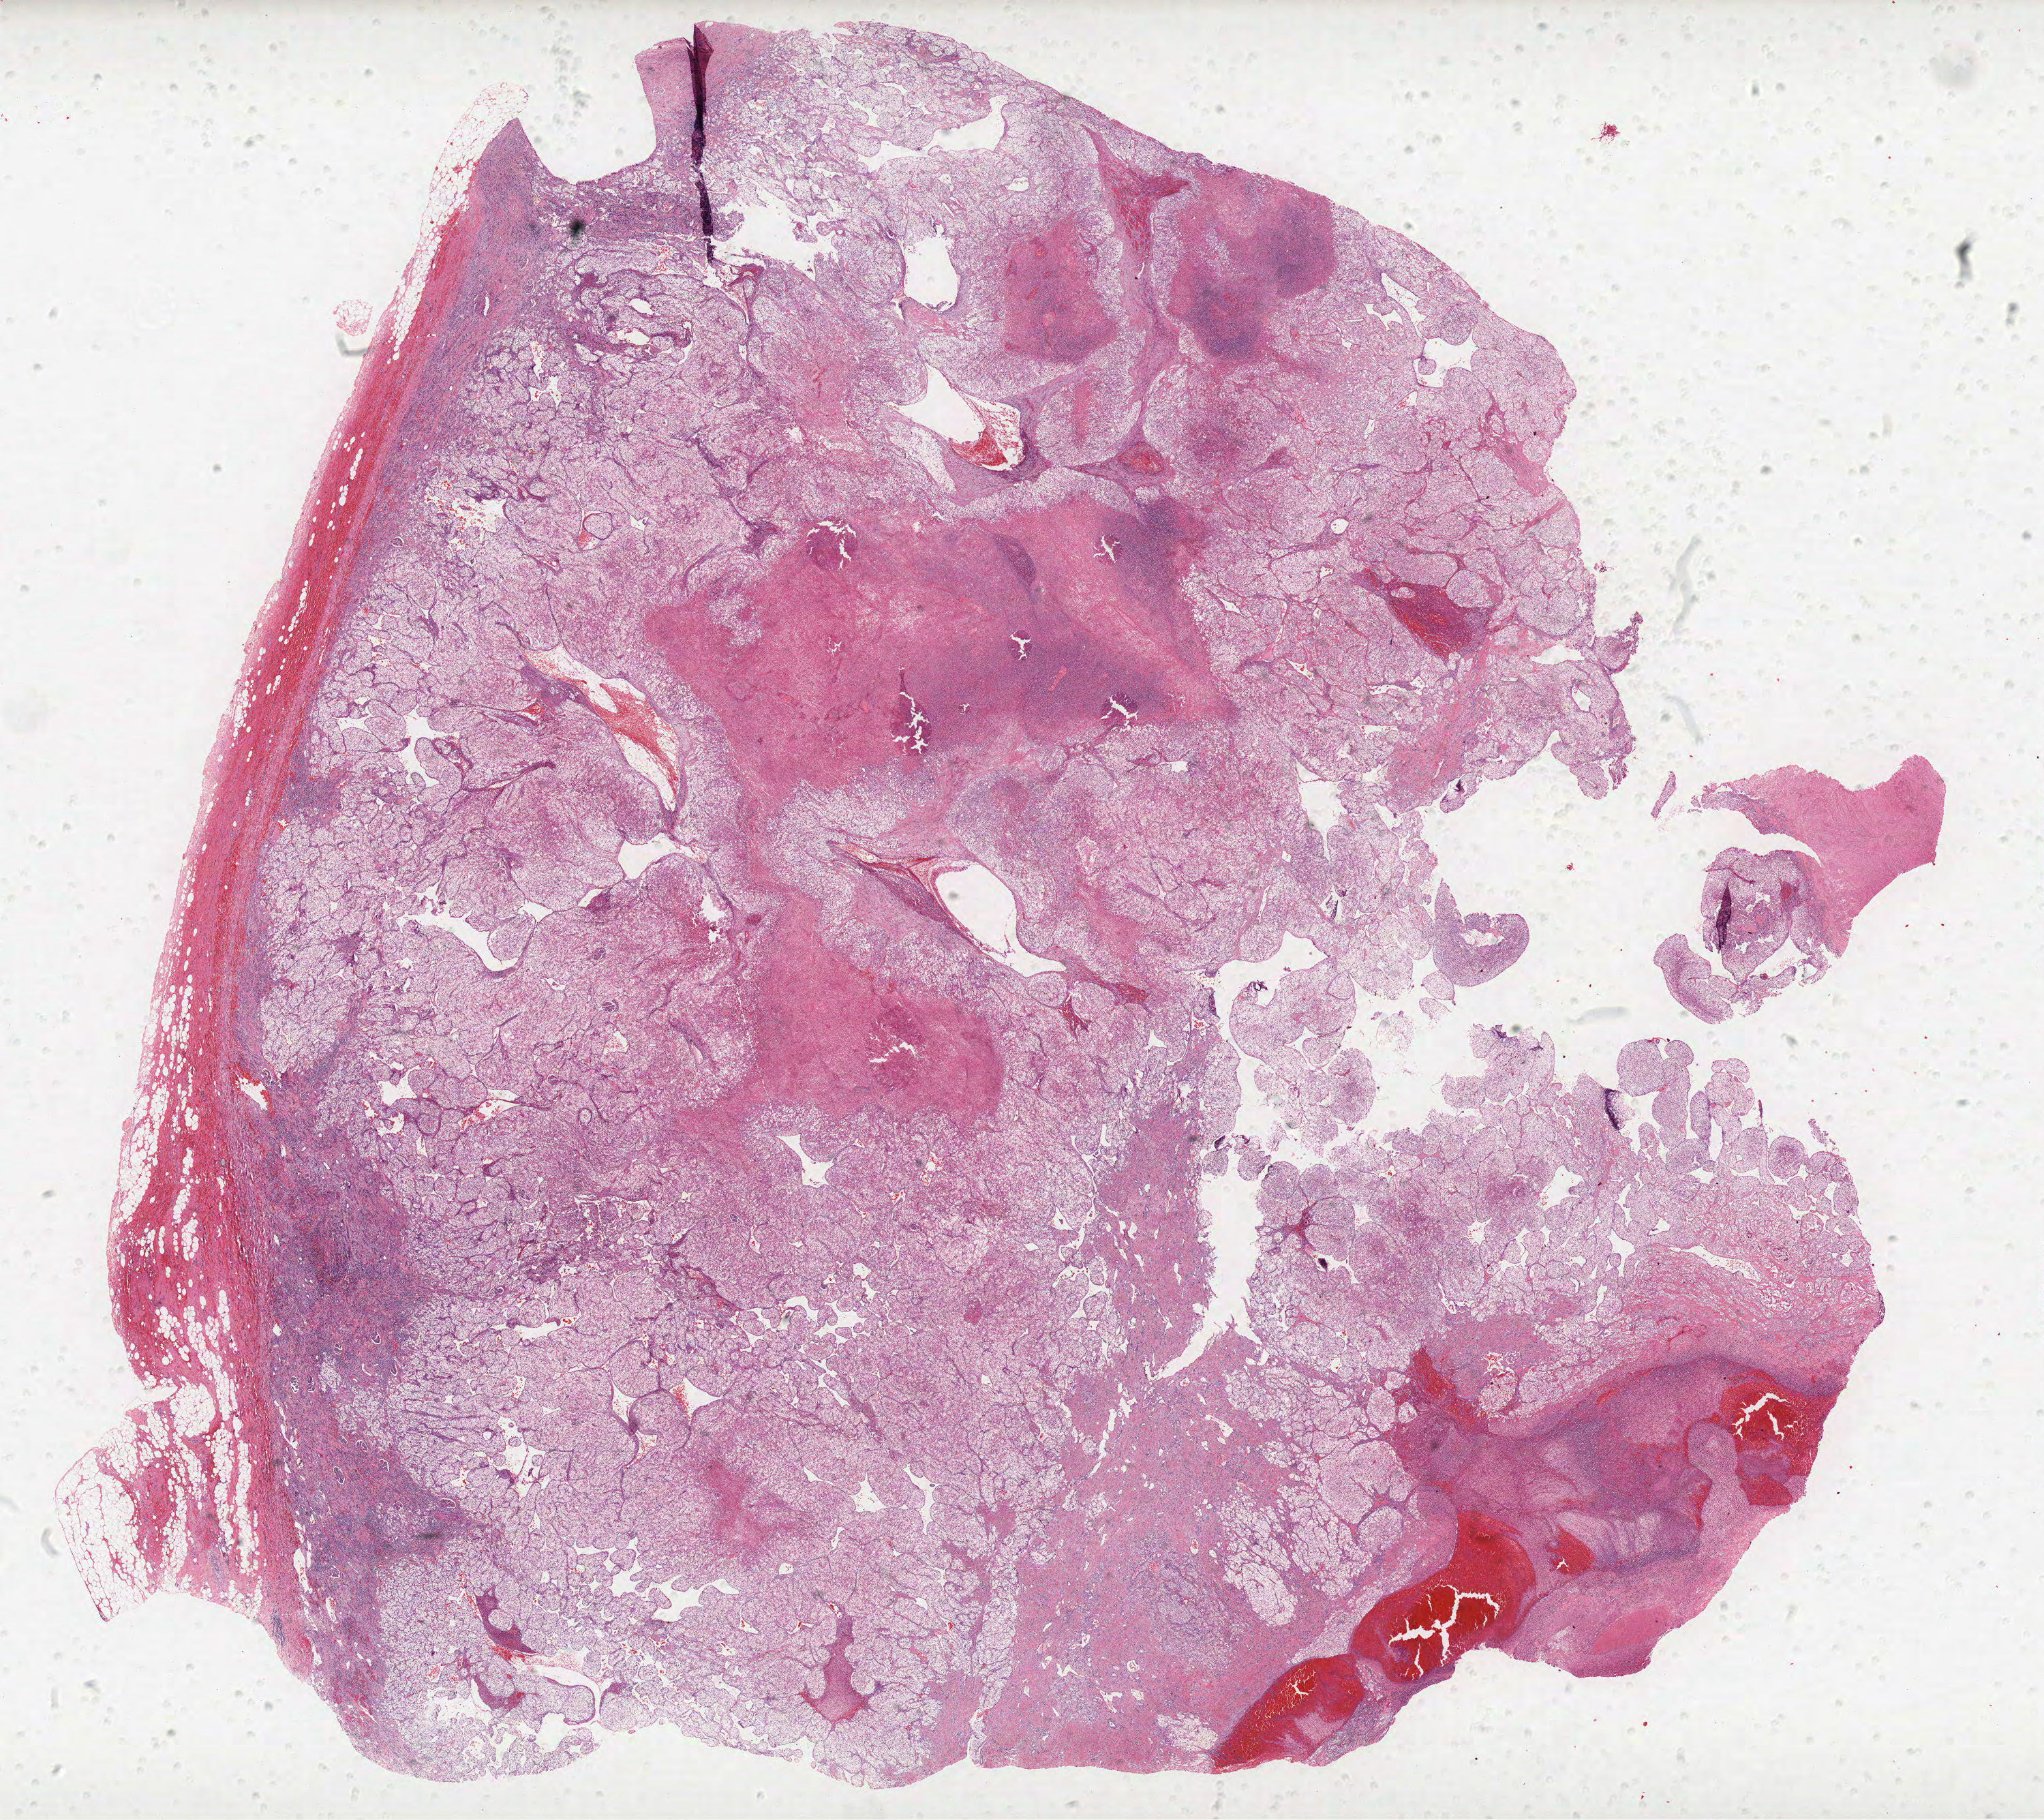
Whole-slide histology image, H&E — low-resolution overview of the scanned area, about 24.0 x 21.3 mm (acquisition: 40x scan), FFPE section, primary tumour sample from the kidney. Male patient; age at initial diagnosis 75 years. Histologic grade: G2 (moderately differentiated).
Histologic diagnosis: Clear cell adenocarcinoma, NOS. AJCC pathologic stage: III. Laterality: right.